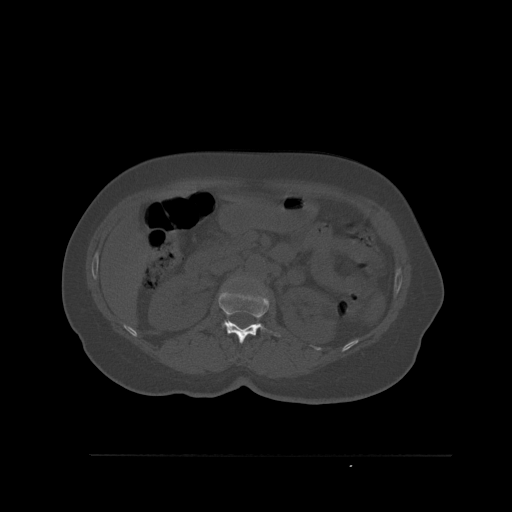
CT including the spine, one axial slice. Position 263 of 527 along the scan axis. Bone window (W 1800 / L 400 HU). 512 × 512 image matrix. Female patient, age 73 years. From the clinical record (not read from this slice): primary cancer: breast; vertebrae with lytic lesions (as recorded): L2.
Outlined on this slice (semi-automatic segmentation, software-assisted and operator-edited):
- L1 vertebra: bounding box [x1, y1, x2, y2] px = [211, 289, 281, 343]